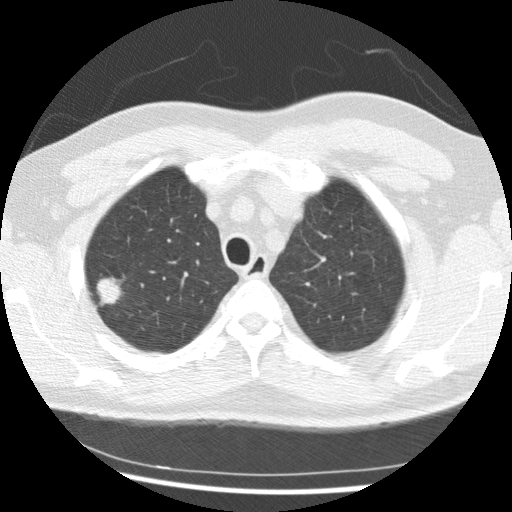
Low-dose screening chest CT, axial slice. First (baseline) screen. Lung window (W 1500 / L -600 HU). Standard (soft-tissue) reconstruction kernel (STANDARD). Slice 52 of 265 in the series. 512 × 512 image matrix, field of view 340 × 340 mm. Male participant, aged 56 years at enrolment.
Lesion marked by an expert reader, bounding box <82,272,131,315> (left, top, right, bottom; pixels). The exam's reader record, not a measurement of the box and not confirmed to be the same lesion: non-calcified nodule or mass ≥4 mm, right upper lobe, 19 × 15 mm, spiculated (stellate) margins, soft tissue attenuation. Official screen result: positive, change unspecified: nodule(s) >= 4 mm or enlarging nodule(s), mass(es), or other non-specific abnormalities suspicious for lung cancer. Lung cancer was diagnosed 291 days after this screen: non-small cell carcinoma, right upper lobe, poorly differentiated (G3), stage IIIB (AJCC 6th edition), 20 mm at pathology.